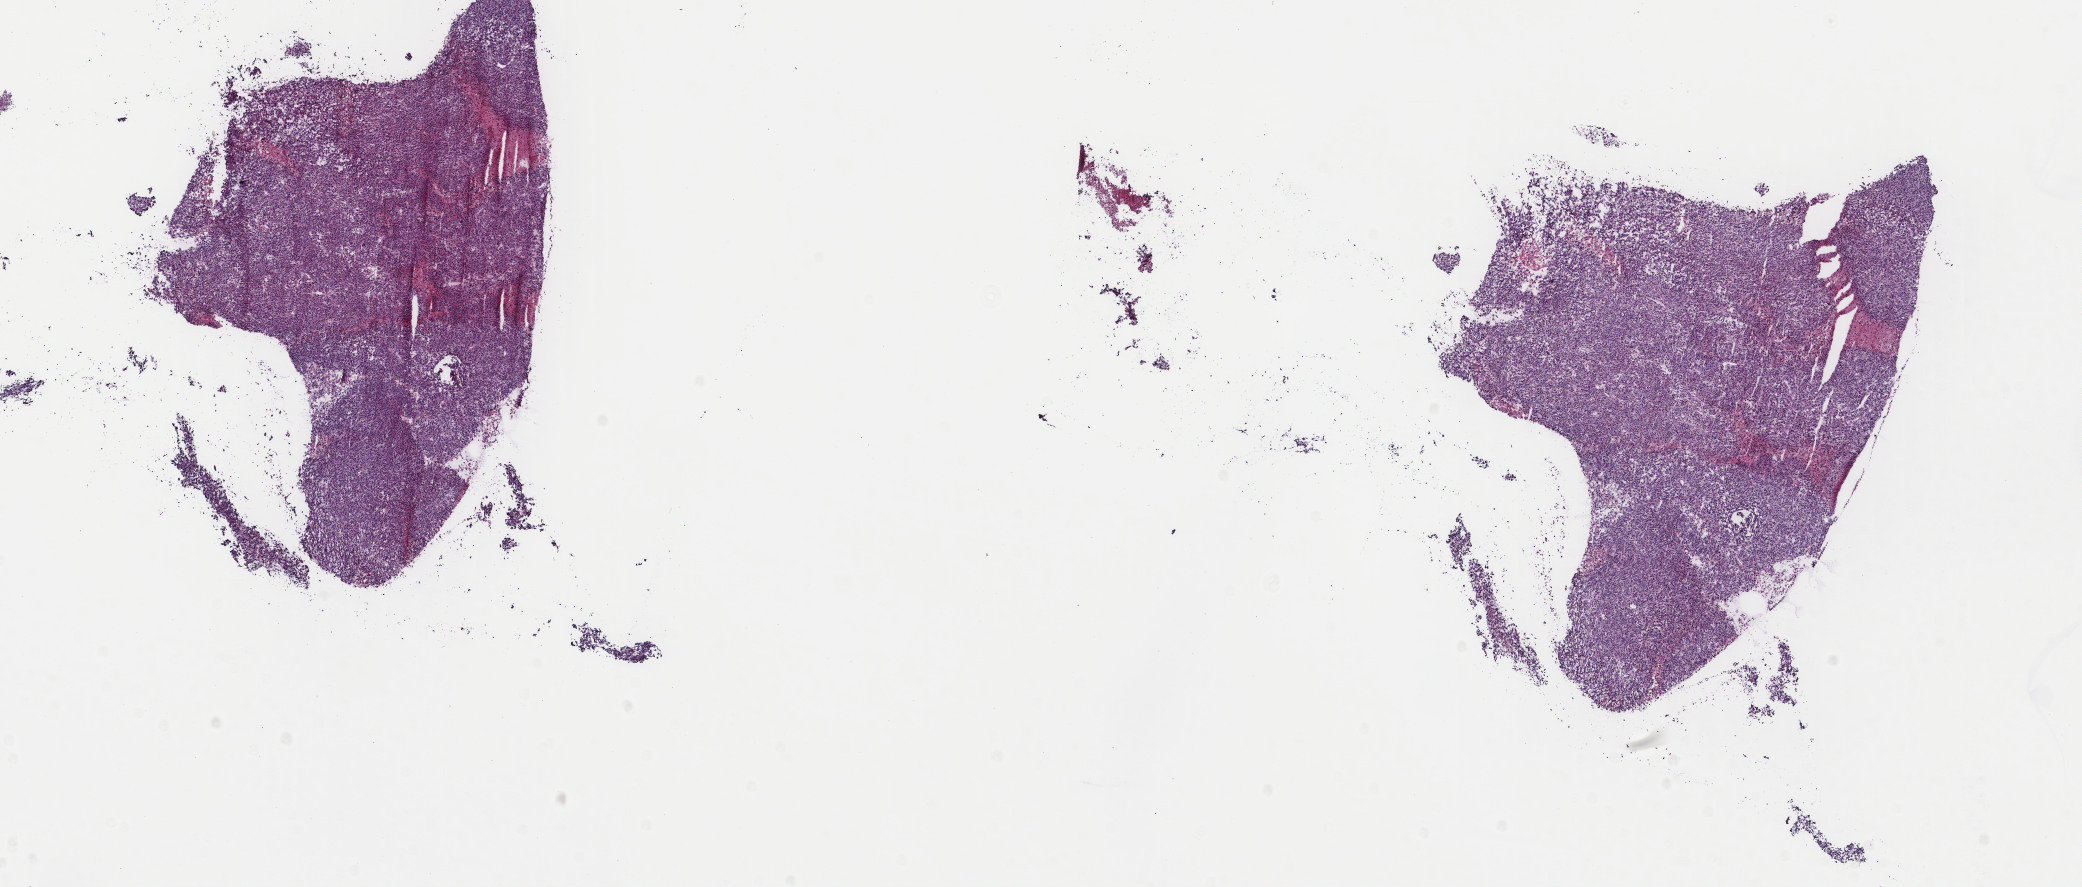
Digitized Hematoxylin and eosin (H&E) stained tissue section (whole slide), a low-resolution overview of the entire scanned area, about 16.5 x 7.0 mm, frozen section from the top of the tissue portion, primary tumour sample from the uterus. Patient: female, age at initial diagnosis 58 years. Slide review estimates, as recorded: tumour cells 85%, tumour nuclei 100%, normal cells 0%, stromal cells 5%, necrosis 10%. Inflammatory infiltration, as recorded: lymphocyte infiltration 0%, monocyte infiltration 0%, neutrophil infiltration 0%.
Diagnosis: Leiomyosarcoma, NOS.